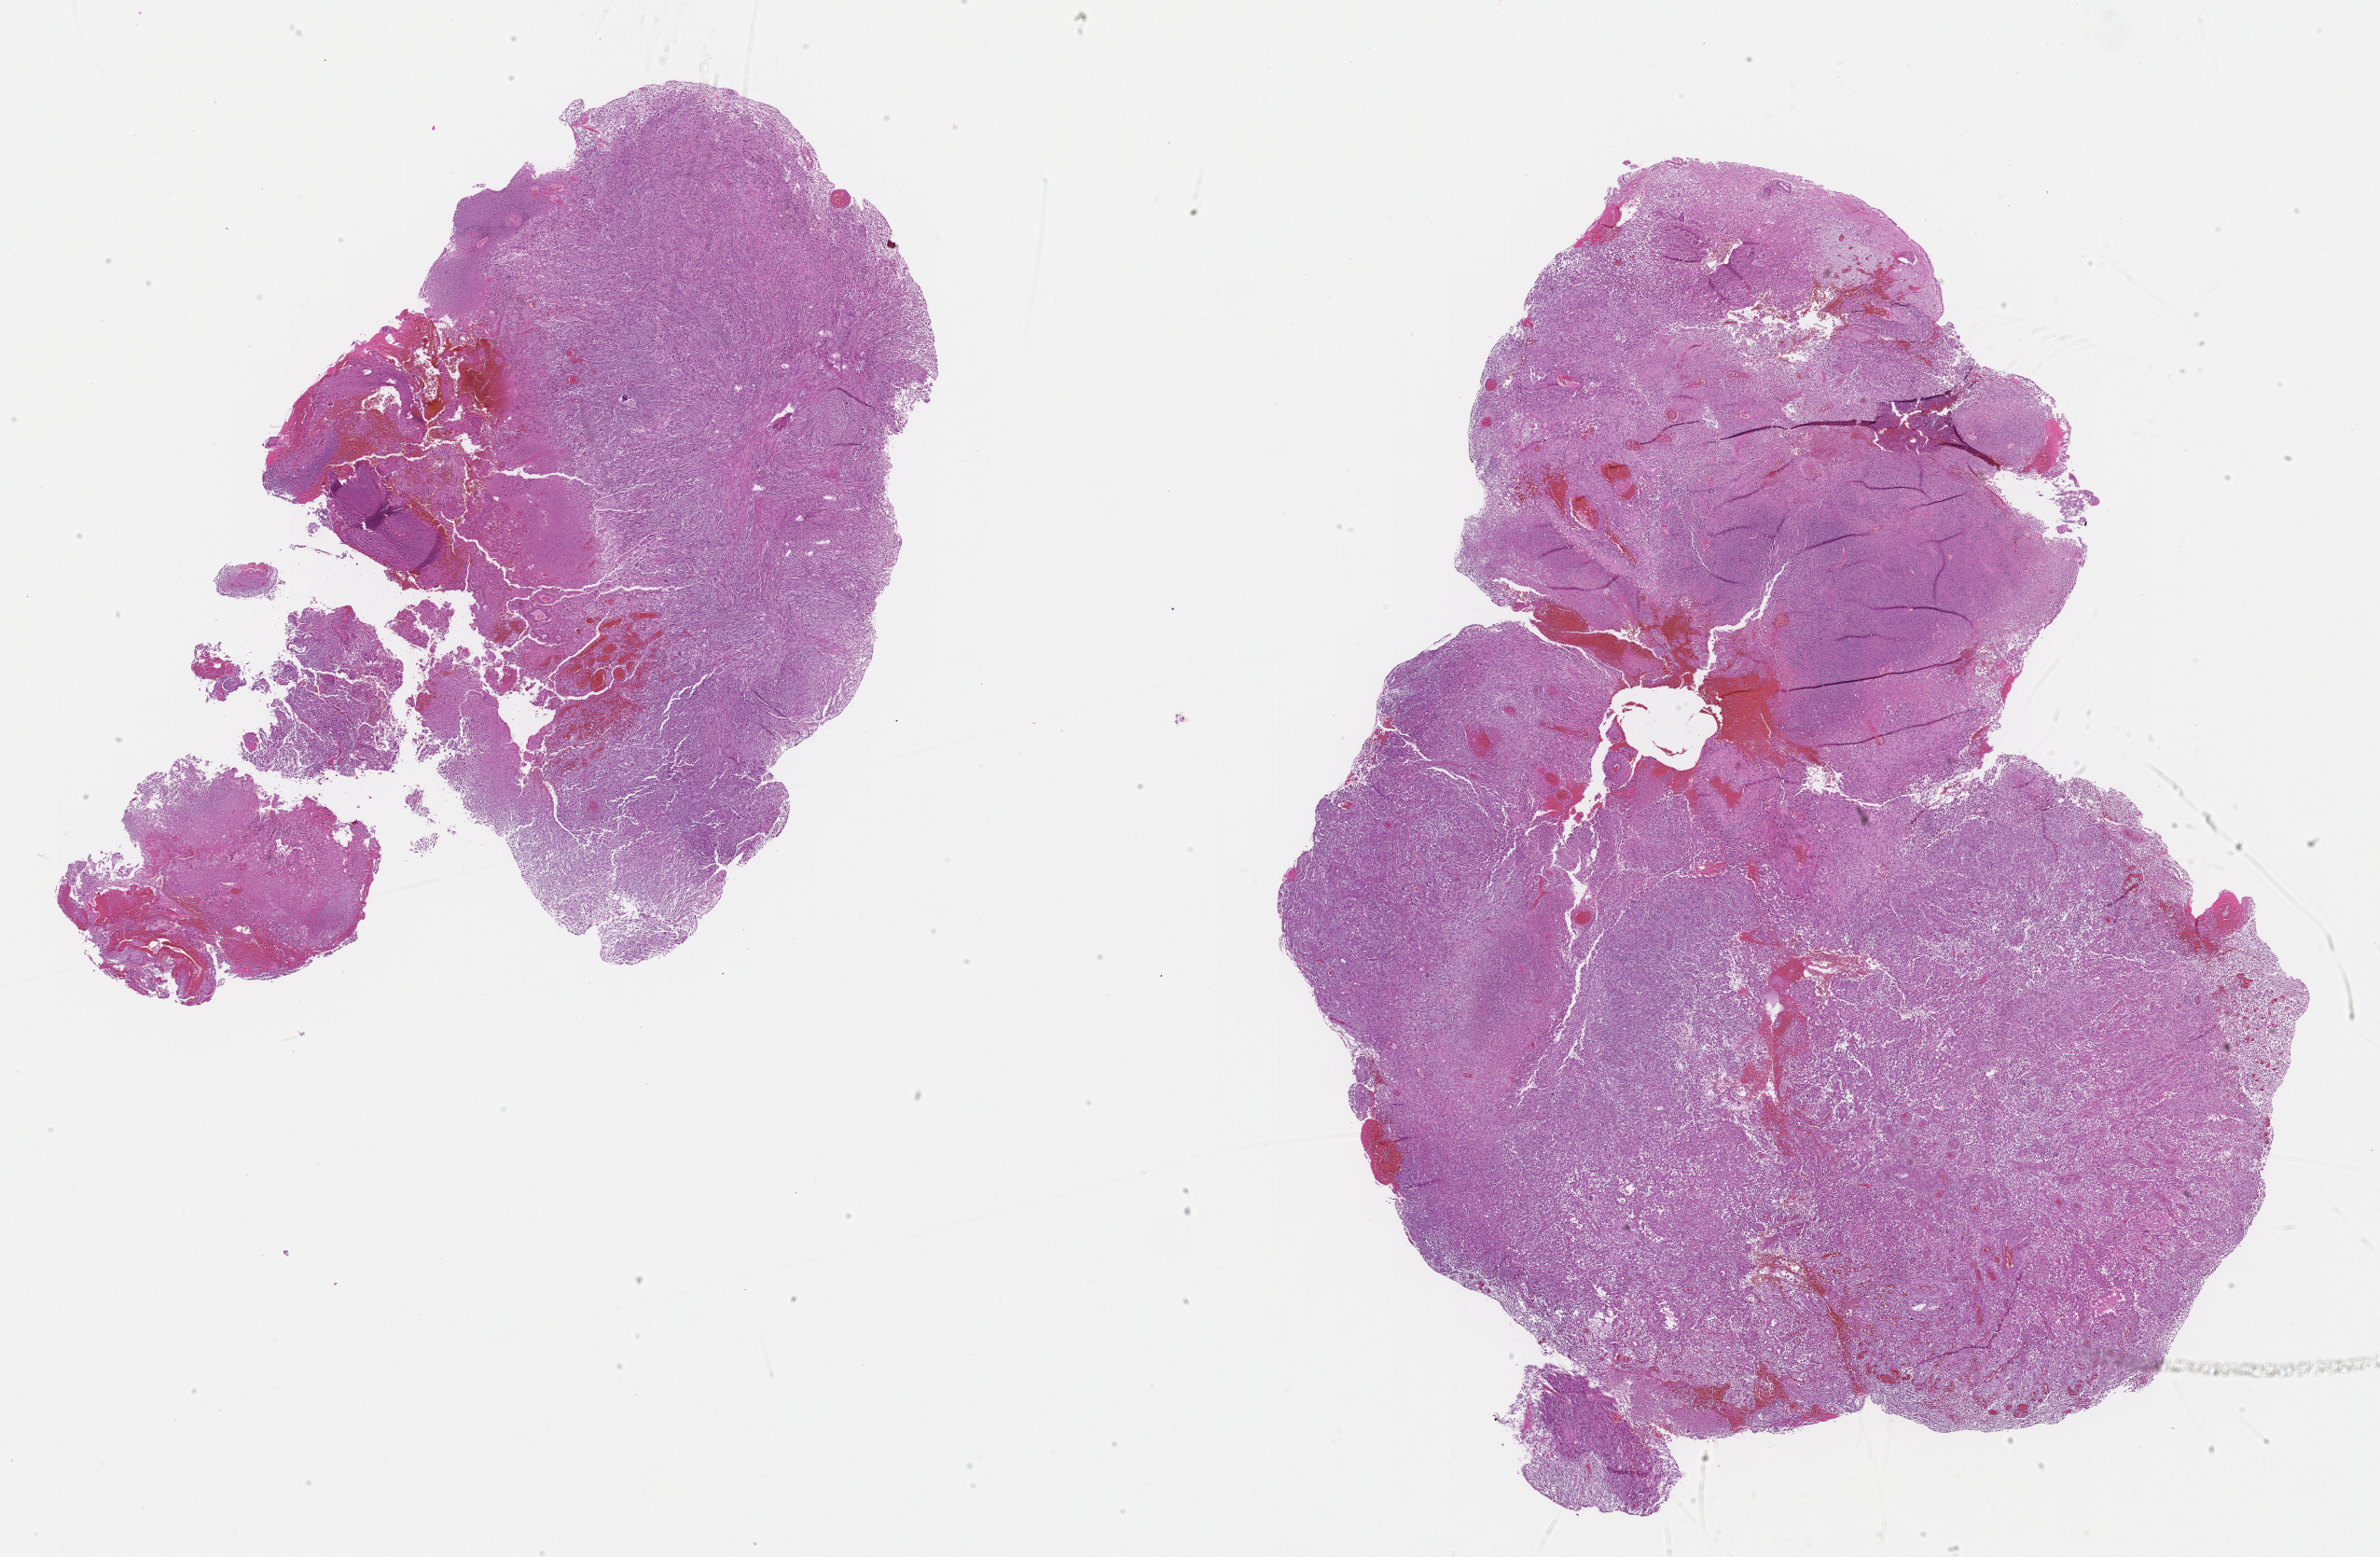
H&E whole-slide image, a low-resolution overview of the entire scanned area, about 20.7 x 13.5 mm (from a 40x scan); FFPE section; brain, primary tumour sample. Patient: male, age at initial diagnosis 63 years.
Pathologic diagnosis: Glioblastoma.